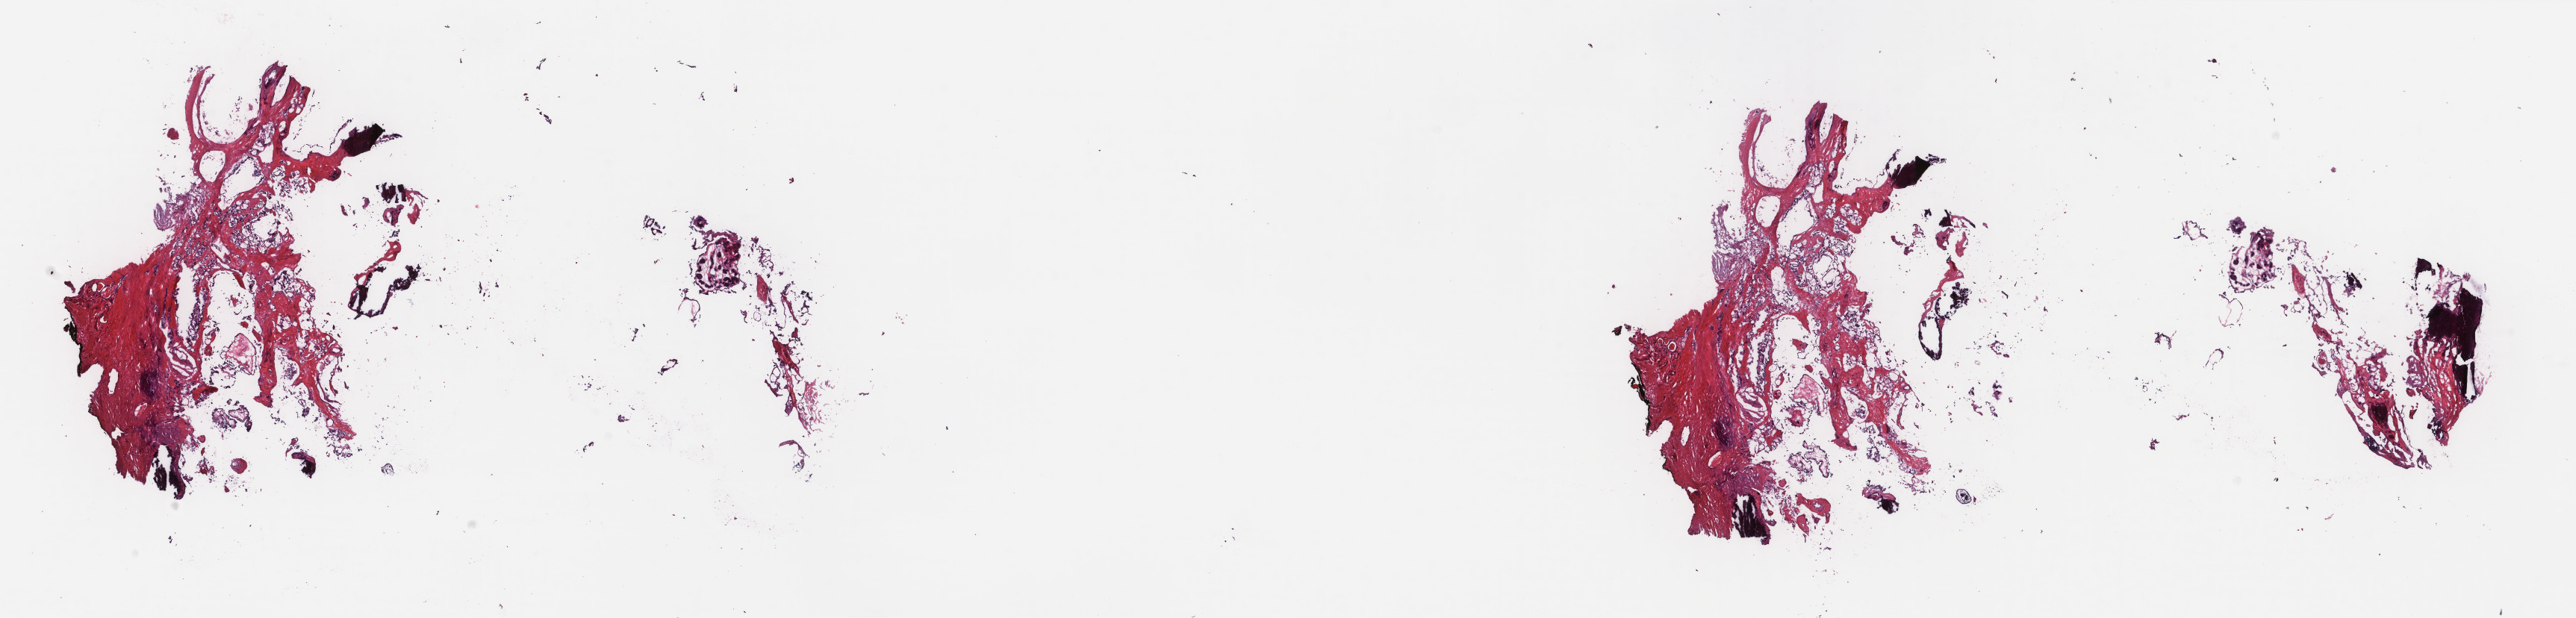
Hematoxylin and eosin (H&E) stained whole-slide image — low-resolution overview of the scanned area, about 27.4 x 6.6 mm. Frozen section from the top of the tissue portion. Thyroid, primary tumour sample. Female, age 70 years at initial diagnosis. Slide review estimates, as recorded: tumour cells 70%, tumour nuclei 80%, normal cells 5%, stromal cells 25%, necrosis 0%. Inflammatory infiltration, as recorded: lymphocyte infiltration 0%, monocyte infiltration 0%, neutrophil infiltration 0%.
* TNM: T1b N0 M0
* AJCC pathologic stage: I (7th edition)
* histologic diagnosis: Papillary adenocarcinoma, NOS (thyroid gland)